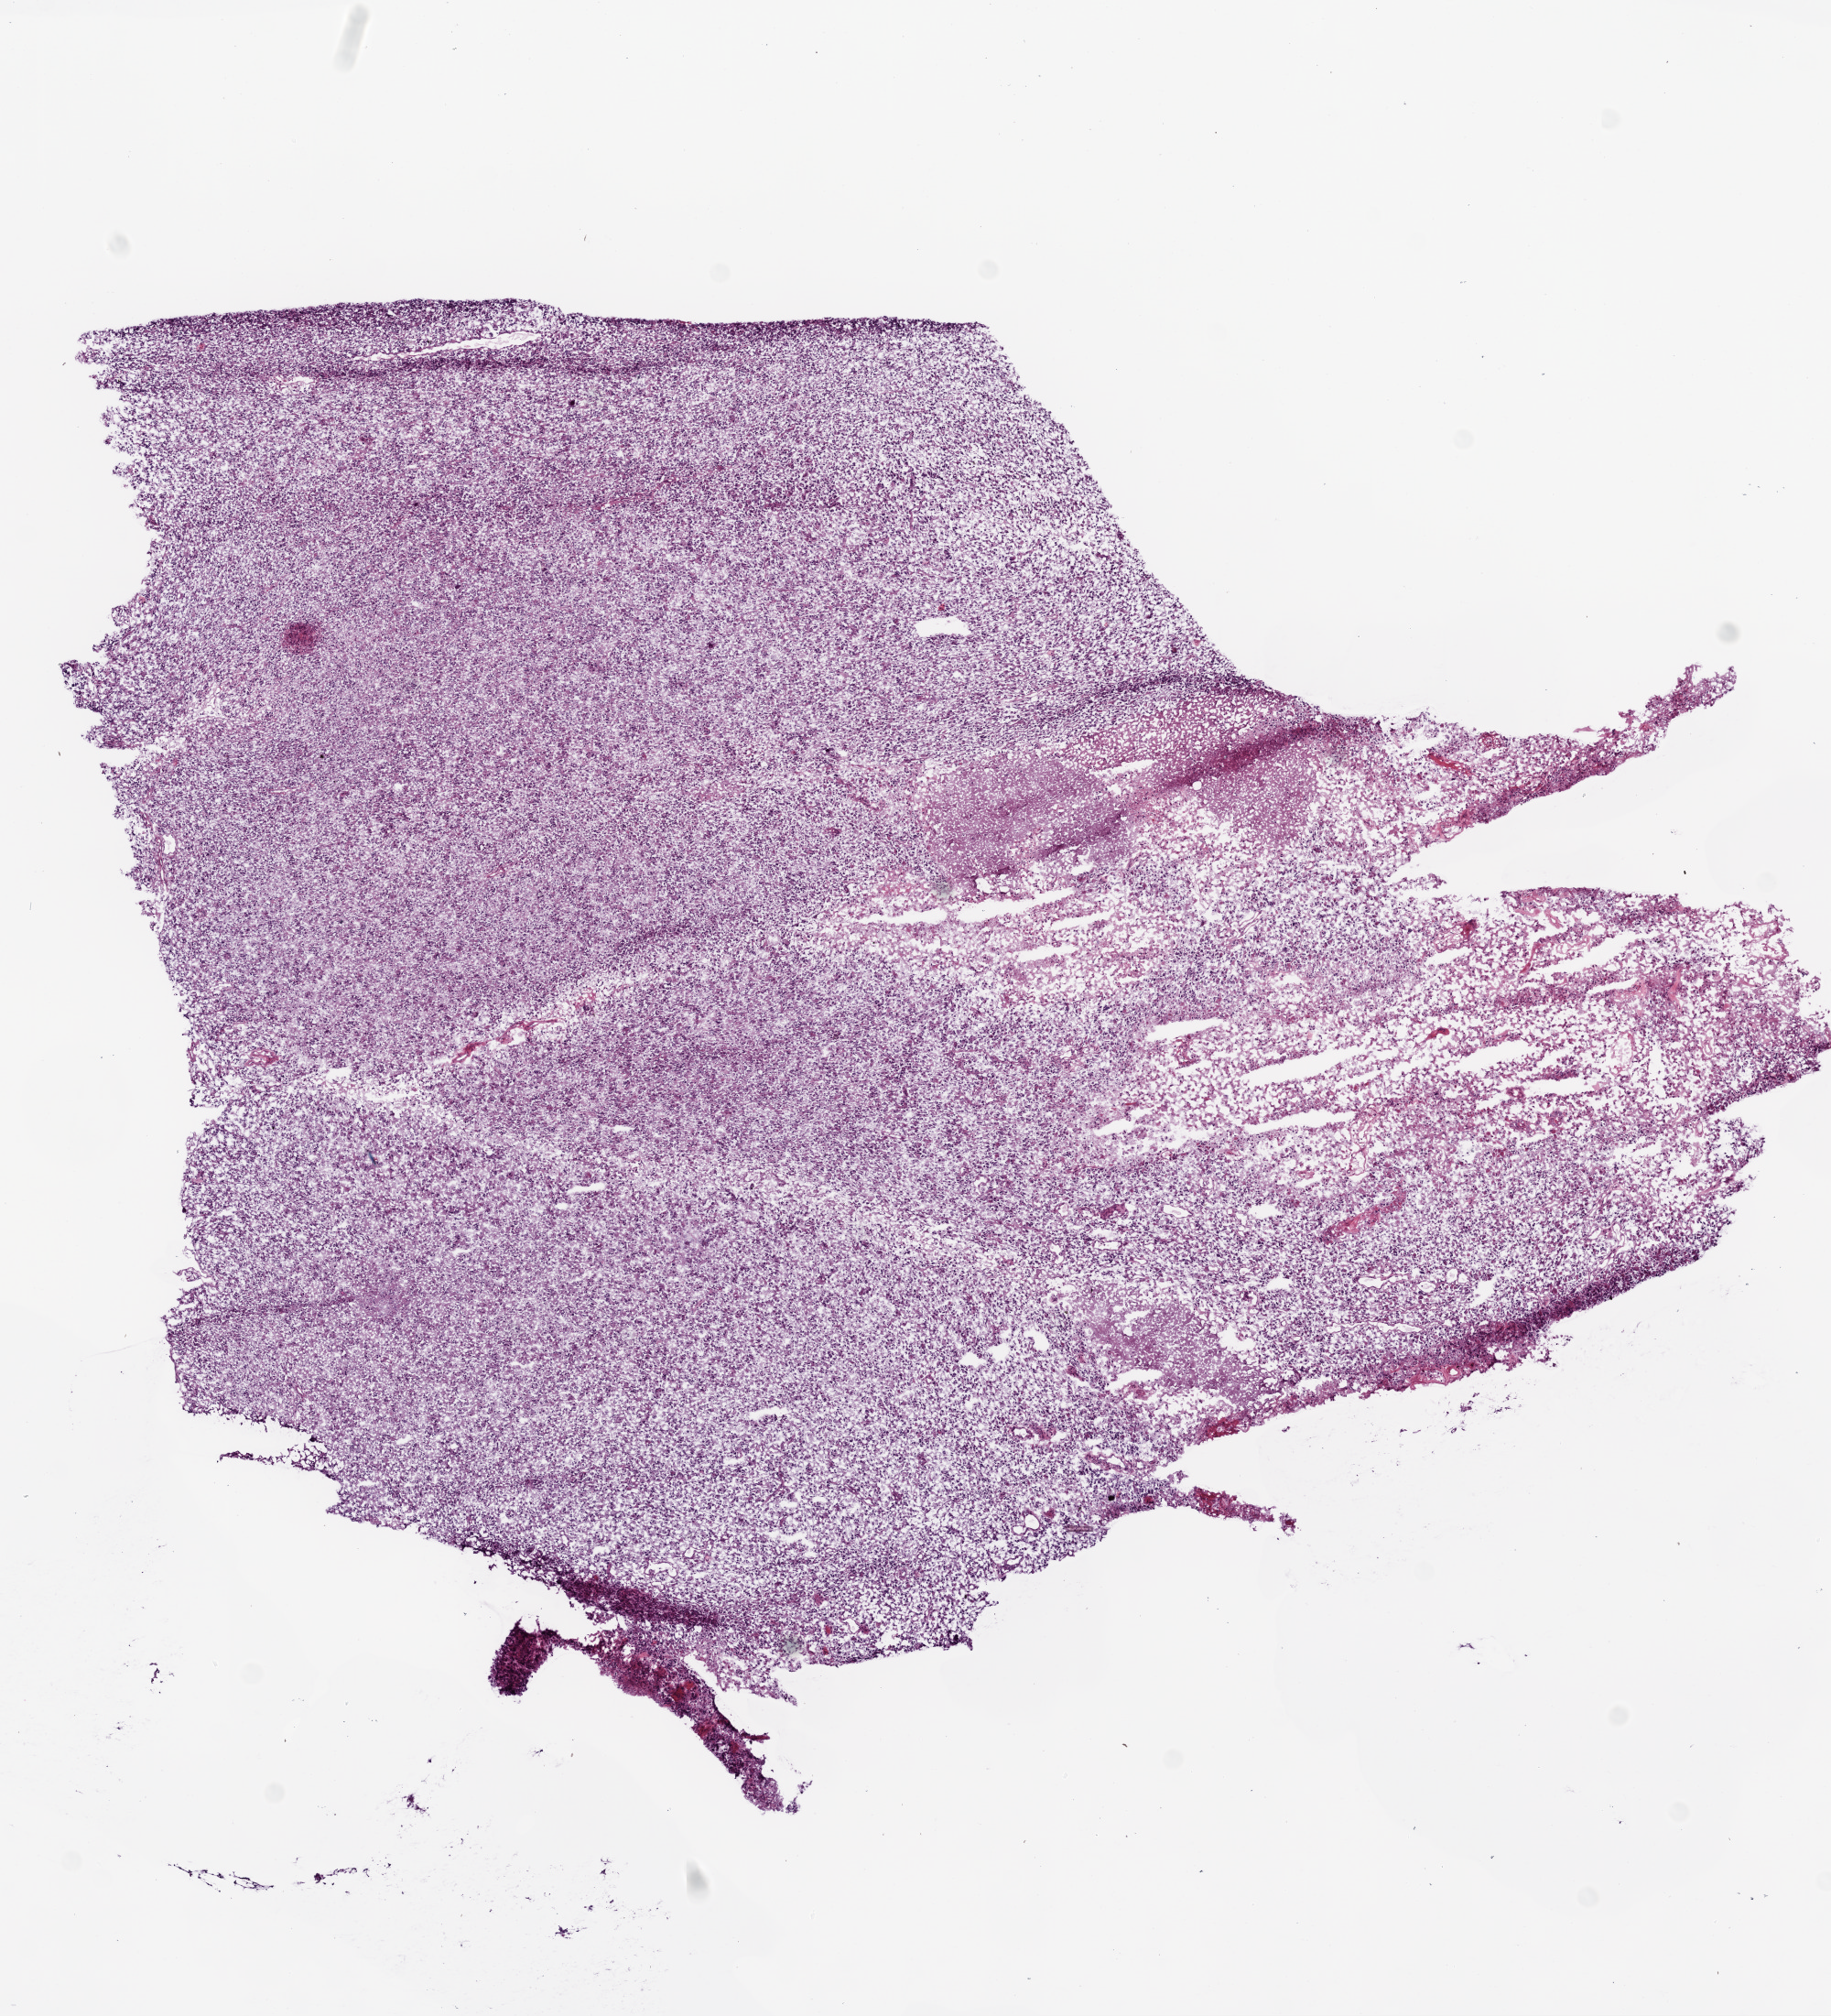
Whole-slide histology image, Hematoxylin and eosin (H&E) stained, shown as a low-resolution overview of the whole scanned area (about 8.0 x 8.8 mm, acquisition: 20x scan), frozen section, sample: primary tumour, brain. Female patient; age at initial diagnosis 77 years. Composition of this section per pathologist review: tumour cells 85%, tumour nuclei 90%, normal cells 0%, stromal cells 0%, necrosis 15%.
• diagnosis: Glioblastoma